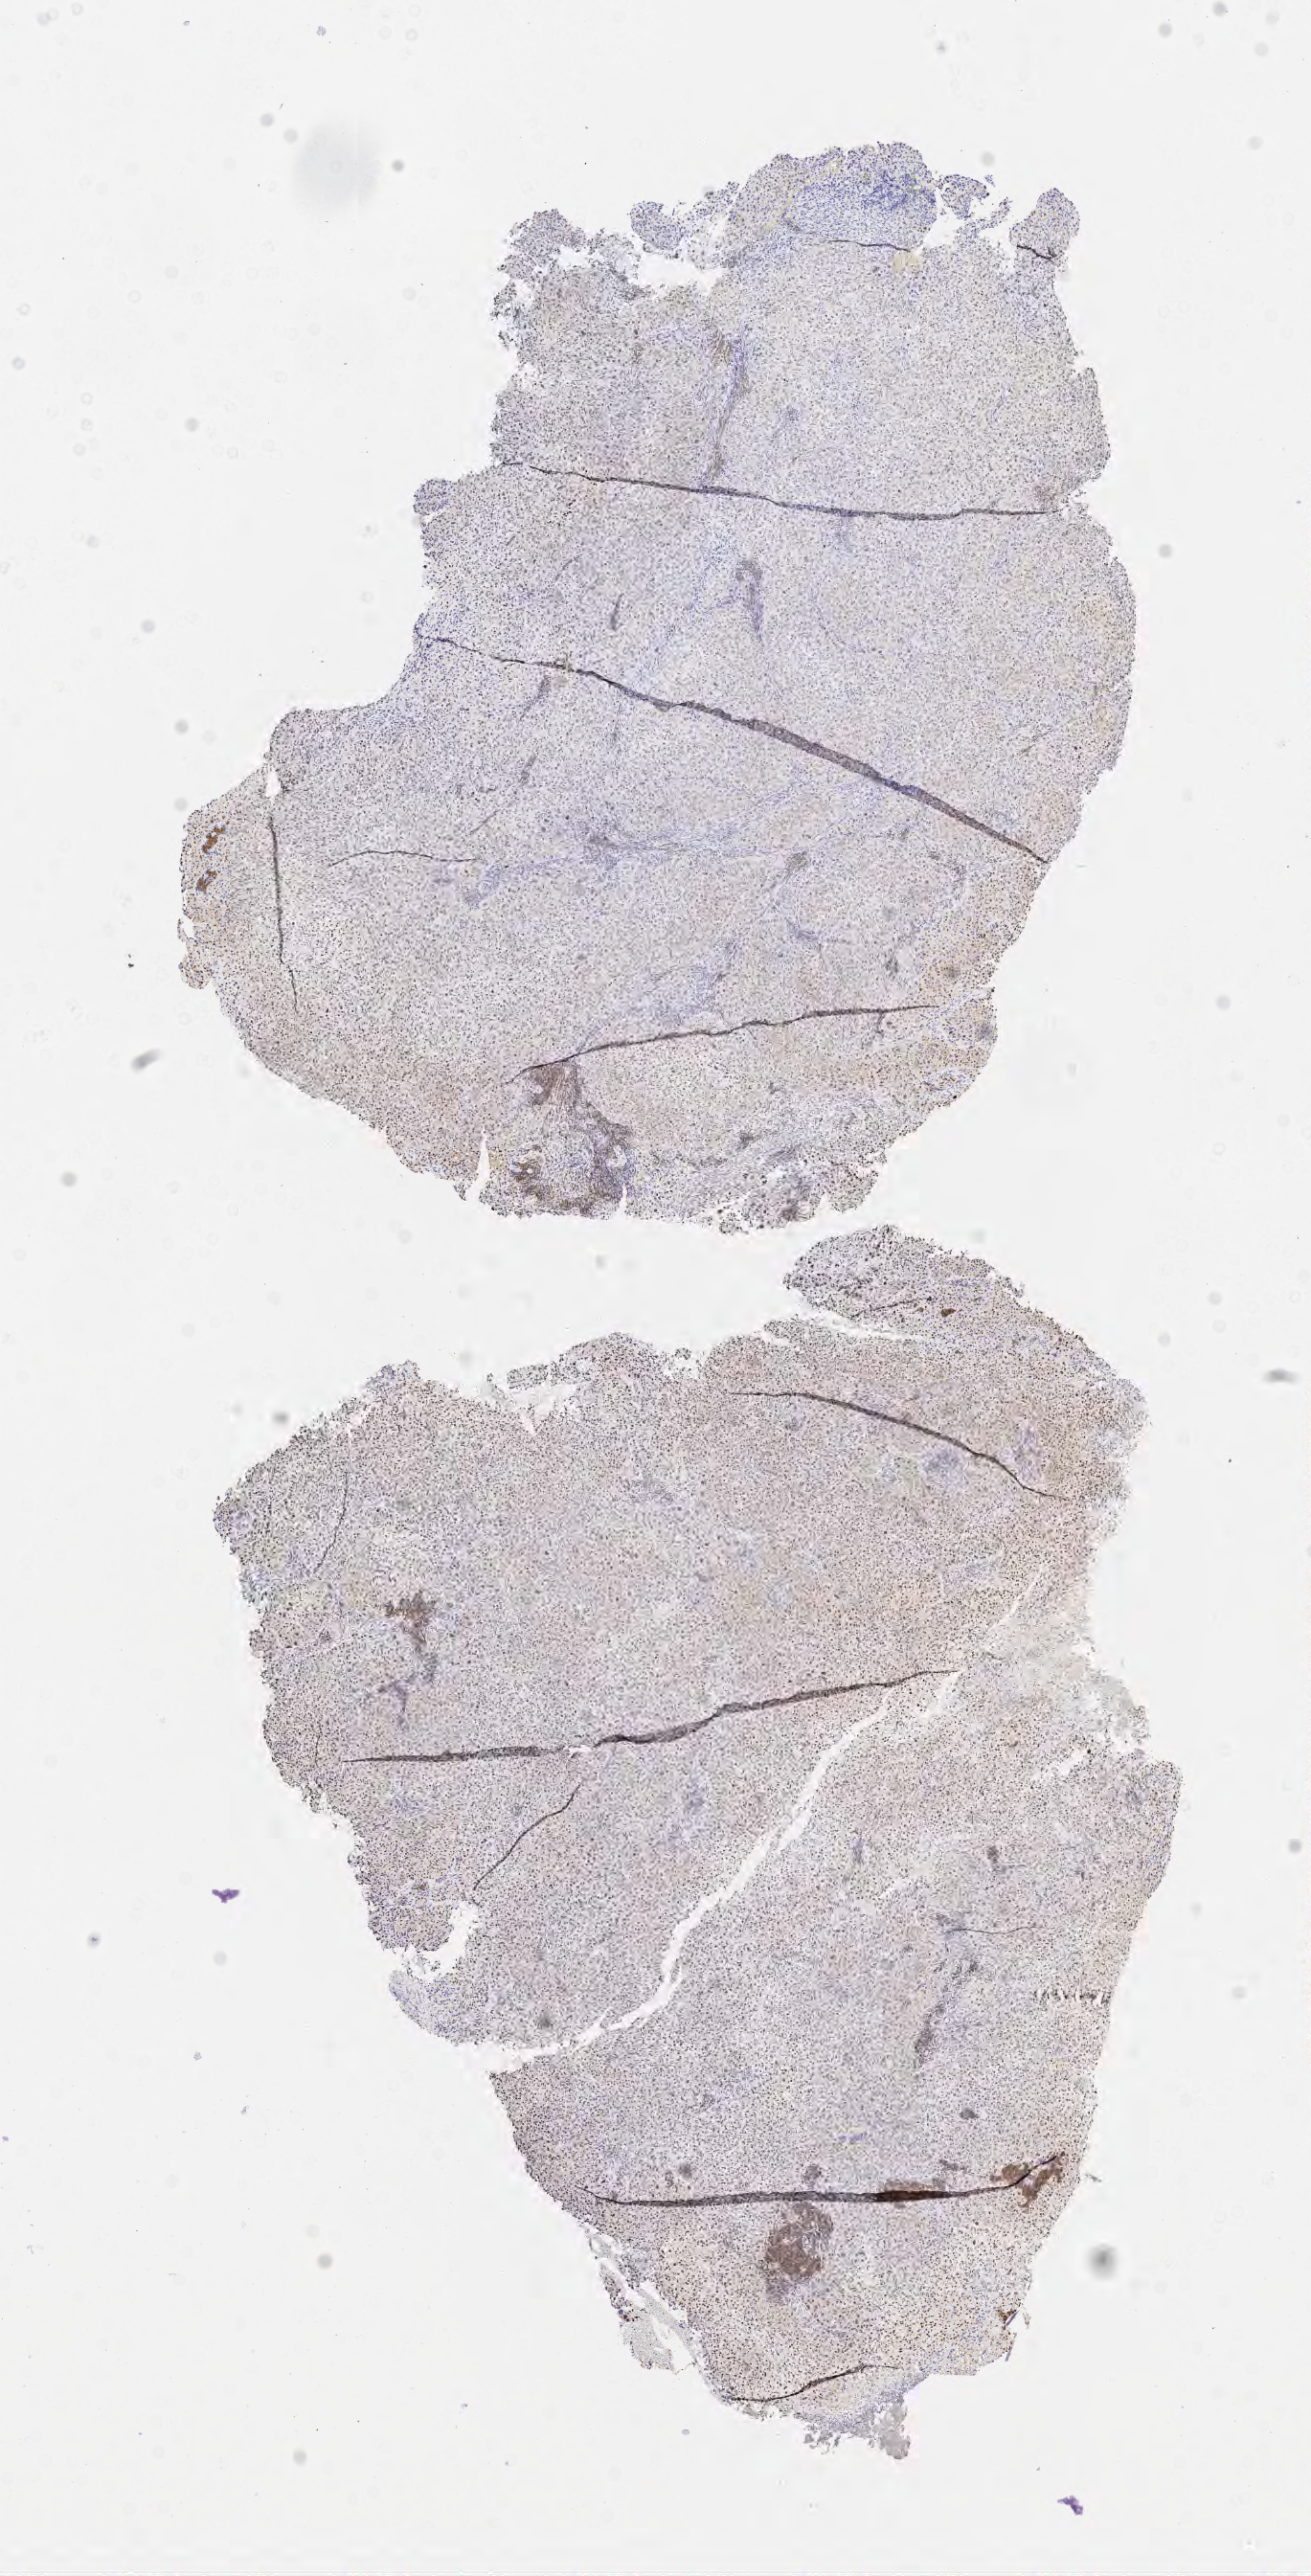
Whole-slide image, immunohistochemical stain for p63 — shown as a low-resolution overview of the whole scanned area (about 5.5 x 10.9 mm), specimen: tumor tissue, site: cervix. Patient: female, 45 years old.
Histologic diagnosis: Squamous cell carcinoma, large cell, nonkeratinizing, NOS.